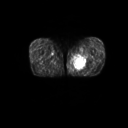
FDG PET of an extremity soft-tissue mass (from a PET/CT study), one axial slice. Slice 16 of 267 in the series (ordered by position). 3.27 mm slice thickness. 128 × 128 image matrix, field of view 600 × 600 mm. Patient: male, 59 years. Case-level facts recorded for this patient, not image findings: histological type: pleiomorphic liposarcoma; grade: high; site of the primary tumour: left thigh.
Annotated regions visible in this slice (expert contour drawn on MRI and transferred to this co-registered scan by the dataset authors):
- gross tumour volume including surrounding oedema: bounding box (x1, y1, x2, y2) in pixels: (73, 53, 90, 71)
- gross tumour volume (mass): (75, 59, 86, 70)